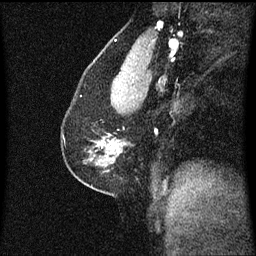
Breast MRI (dynamic contrast-enhanced), one sagittal slice. Position 36 of 60 along the scan axis. Dynamic contrast-enhanced series, image 2 of 3 at this slice position (ordered by acquisition). 1.5 T. TE 4.2 ms, TR 8.4 ms. 2 mm slice thickness. 256 × 256 image matrix, field of view 200 × 200 mm. Female patient, age 41 years. From the clinical record (not read from this slice): setting: breast cancer imaged before/during neoadjuvant chemotherapy; receptor status: triple-negative.
Annotated regions visible in this slice (semi-automatic segmentation, software-assisted and operator-edited):
- analysis volume of interest (the breast-tissue region the enhancement analysis was run in; not a lesion): bounding box [x1, y1, x2, y2] px = [62, 104, 125, 175]
- tumour enhancement mask (voxels above the 70 % enhancement threshold inside the analysis volume of interest): [111, 142, 114, 145]